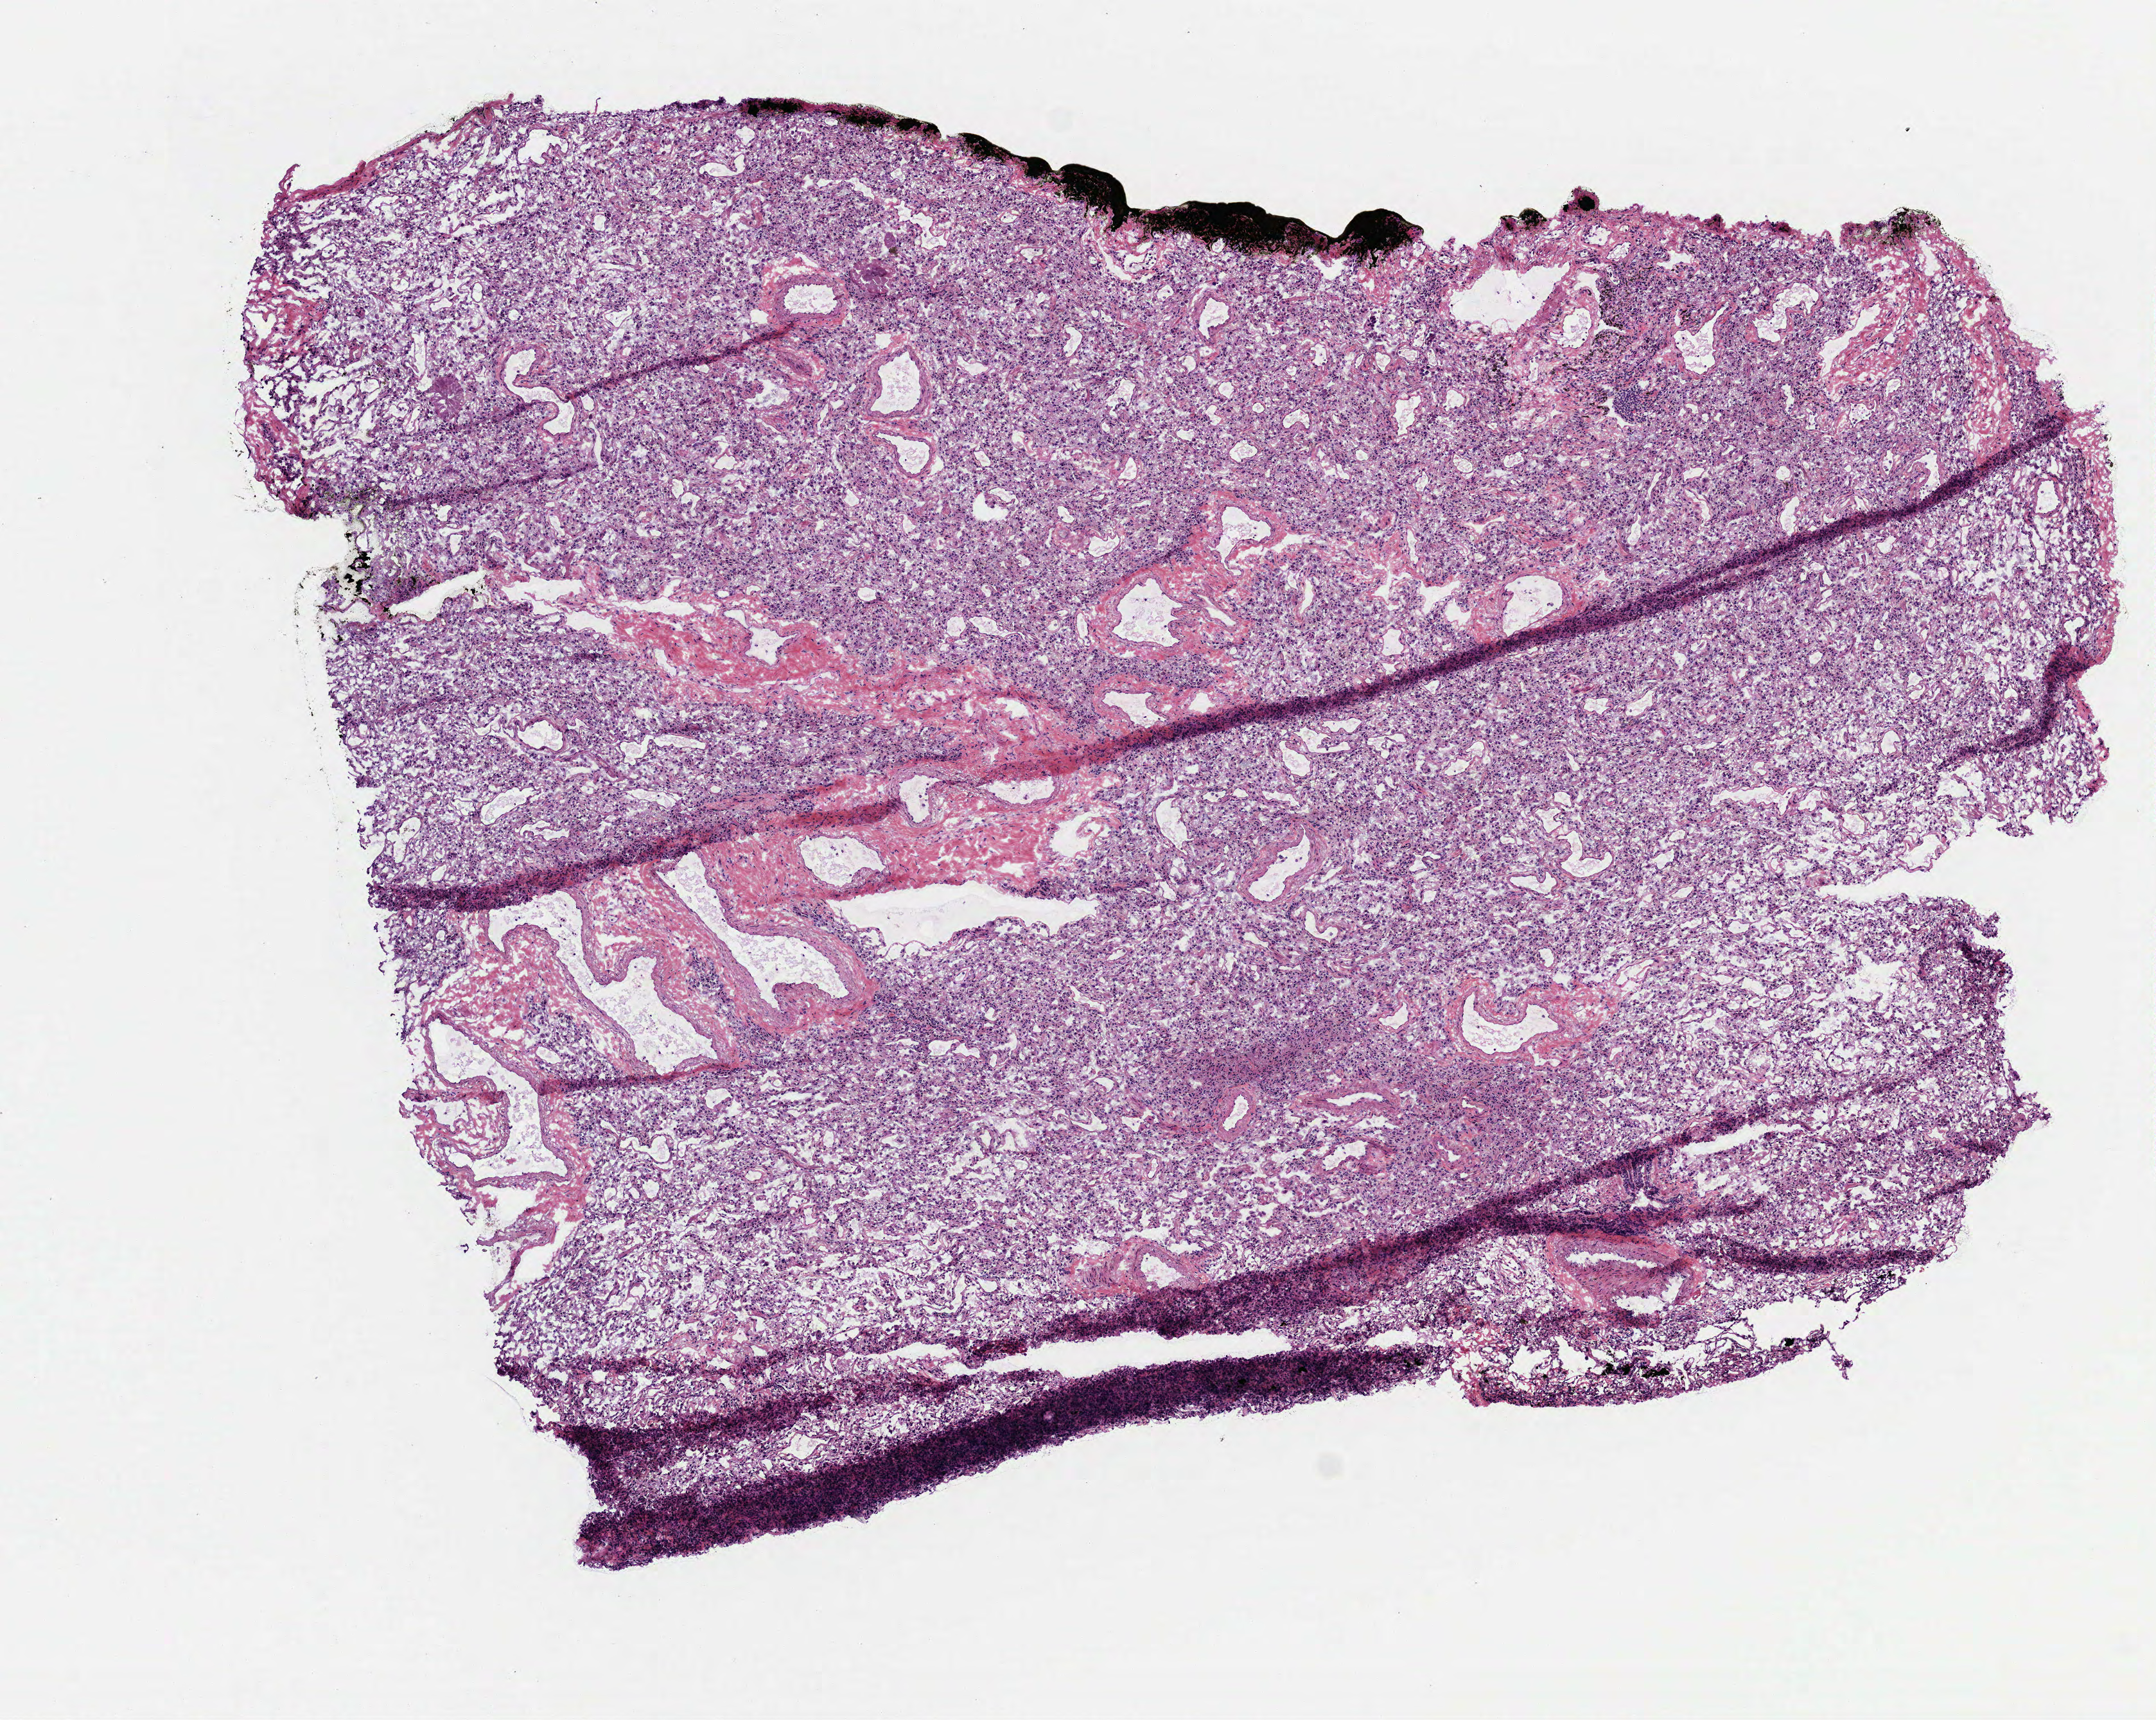
Whole-slide histology image, H&E — whole scanned area (about 6.8 x 5.4 mm) shown as a low-resolution overview; frozen section from the top of the tissue portion; lung, solid tissue normal (non-tumour tissue) sample. Male, age 65 years at initial diagnosis. Infiltration values recorded for this section: lymphocyte infiltration 20%, monocyte infiltration 0%, neutrophil infiltration 20%.
This section: solid tissue normal (non-tumour) sample from the same patient. Patient diagnosis: Squamous cell carcinoma, NOS.